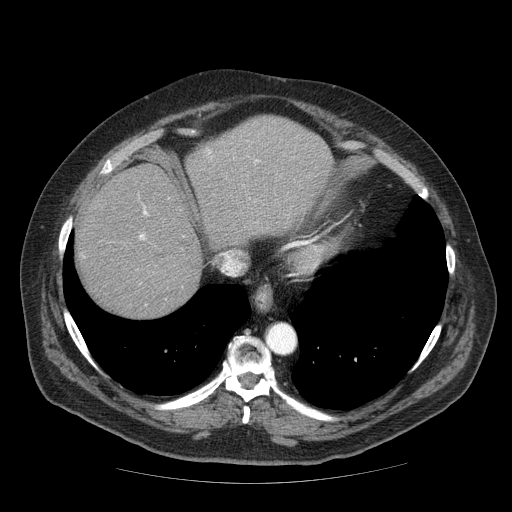
Contrast-enhanced abdominal CT (liver protocol), one axial slice. Slice 59 of 85 in the series (ordered by position). Reconstruction kernel STANDARD. 120 kVp. Soft-tissue window (W 400 / L 40 HU). 512 × 512 image matrix, field of view 420 × 420 mm. Case-level facts recorded for this patient, not image findings: diagnosis: hepatocellular carcinoma (patient treated with transarterial chemoembolisation; whether this scan precedes or follows treatment is not stated here); TNM stage (as recorded): Stage-IIIA; Child-Pugh class: A; tumour nodularity: multinodular; tumour size: 7 cm.
Structures marked on this image (semi-automatically segmented with operator editing):
- abdominal aorta: bounding box [x1, y1, x2, y2] px = [267, 325, 296, 354]
- liver parenchyma outside the tumour (the mass and vessels are separate outlines, so this box may not span the whole liver): [76, 116, 332, 316]
- liver vessels: [140, 211, 147, 239]